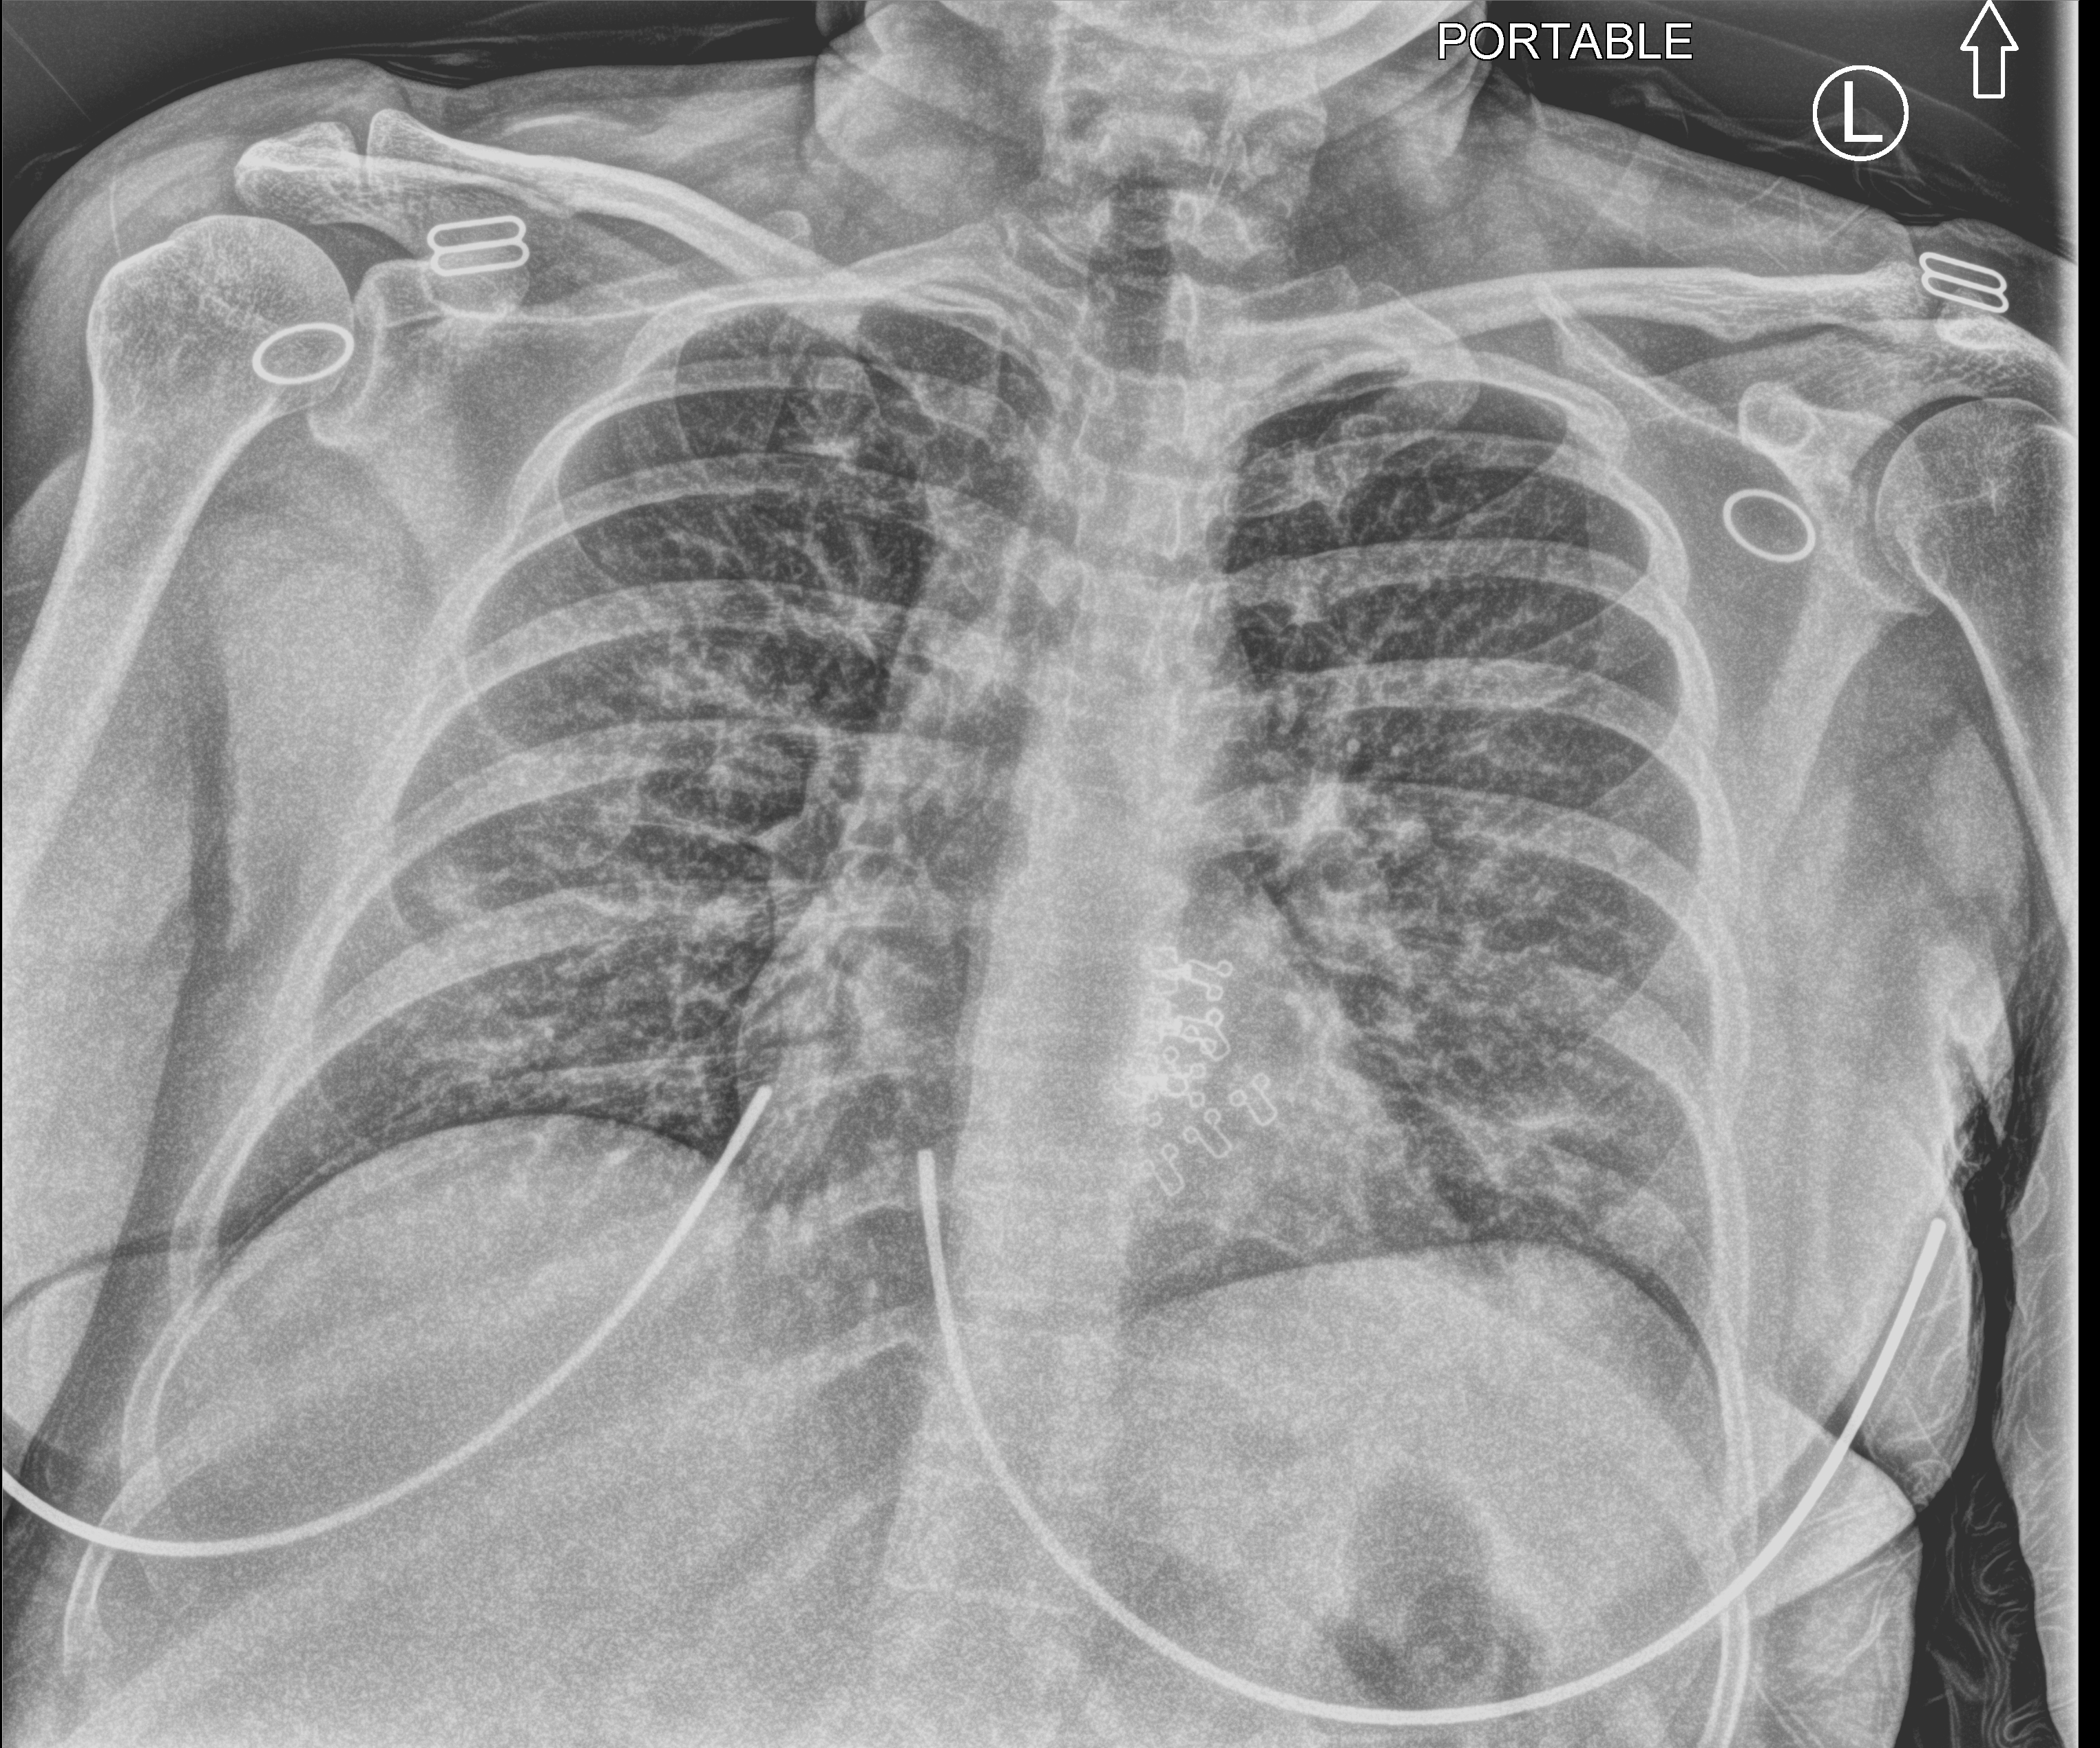
Portable chest radiograph; anteroposterior (AP) projection. Female patient hospitalised with COVID-19, age 18–59 years.
Hospital-stay facts (about this admission, not read from this image; timing relative to this image not recorded):
- length of hospital stay: 2 days
- smoking status (admission record): never